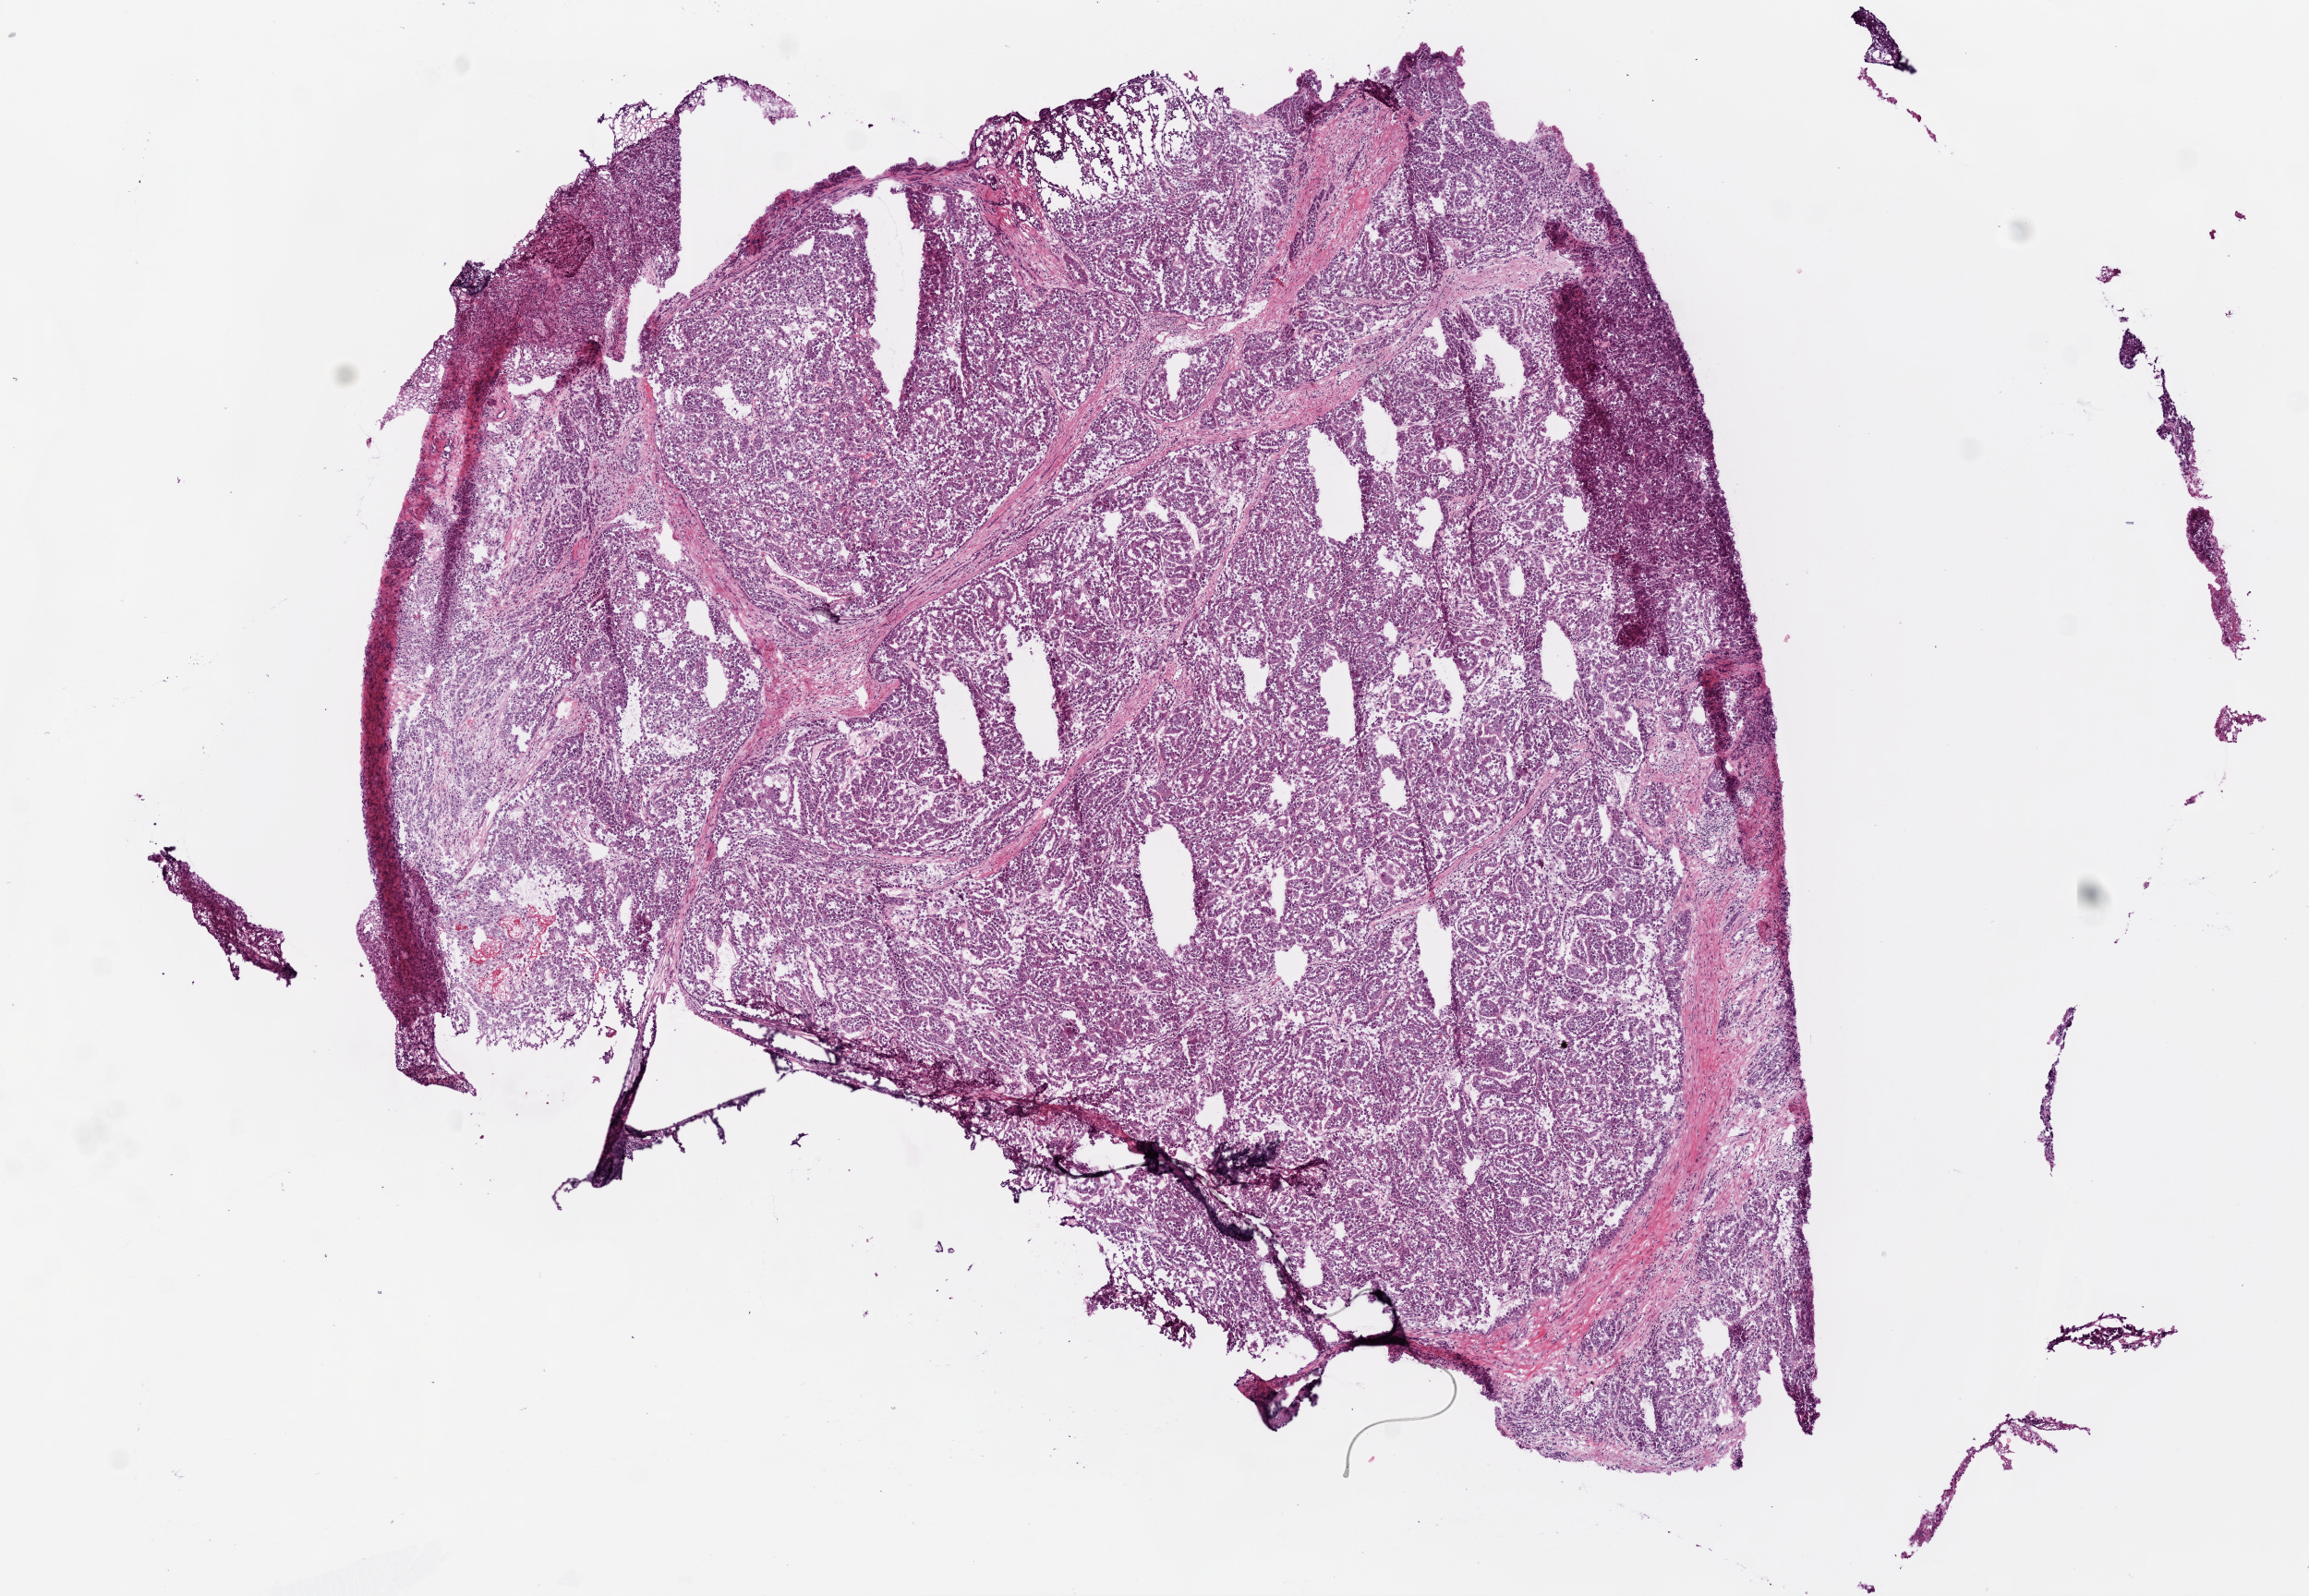
Whole-slide histology image, Hematoxylin and eosin (H&E) stained — whole scanned area (about 10.0 x 6.9 mm, acquisition: 20x scan) shown as a low-resolution overview, frozen section from the bottom of the tissue portion, sample: primary tumour, kidney. Patient: male, age at initial diagnosis 41 years. Composition of this section per pathologist review: tumour cells 90%, tumour nuclei 75%, normal cells 0%, stromal cells 10%, necrosis 5%.
• laterality: right
• TNM: T3b N1 M1
• AJCC pathologic stage: IV
• lymph nodes positive (case pathology): 2 of 2 examined
• histologic diagnosis: Papillary adenocarcinoma, NOS